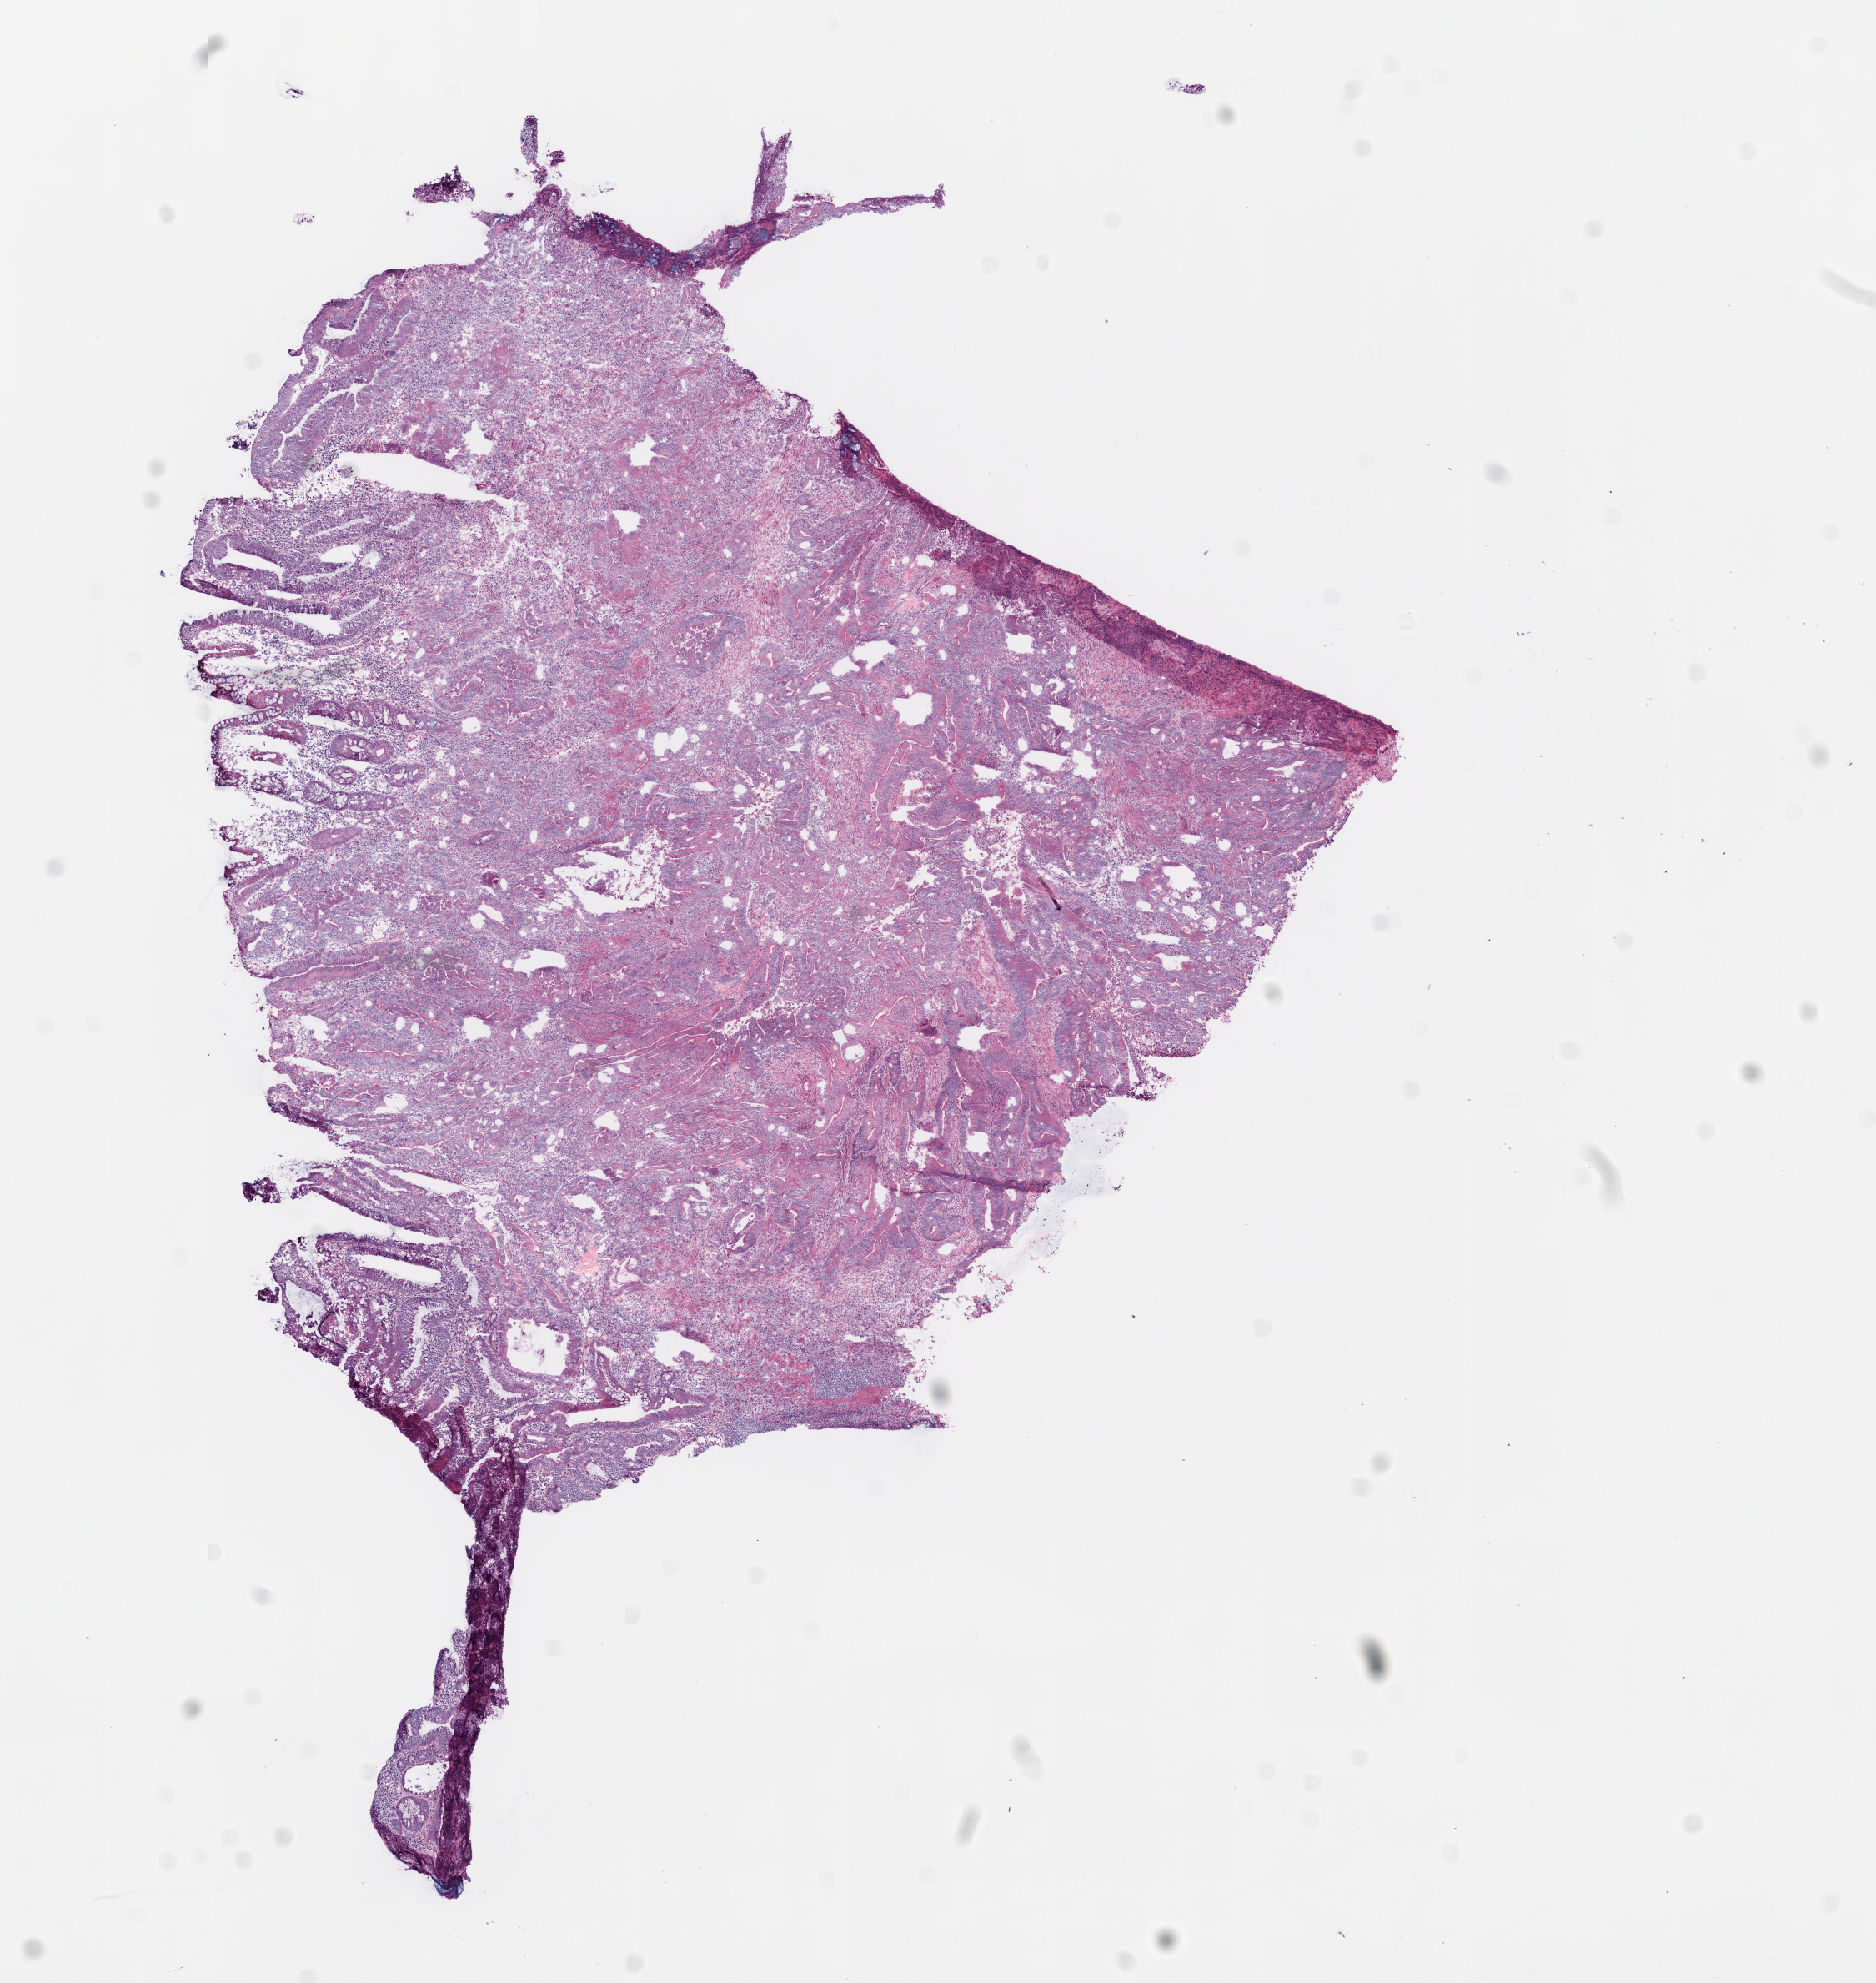
Whole-slide histology image, H&E-stained, shown as a low-resolution overview of the whole scanned area (about 9.0 x 9.5 mm, acquisition: 20x scan); frozen section from the top of the tissue portion; primary tumour sample from the colon. Male, age 67 years at initial diagnosis. Composition of this section per pathologist review: tumour cells 80%, tumour nuclei 90%.
Pathologic diagnosis: Adenocarcinoma, NOS (ascending colon).